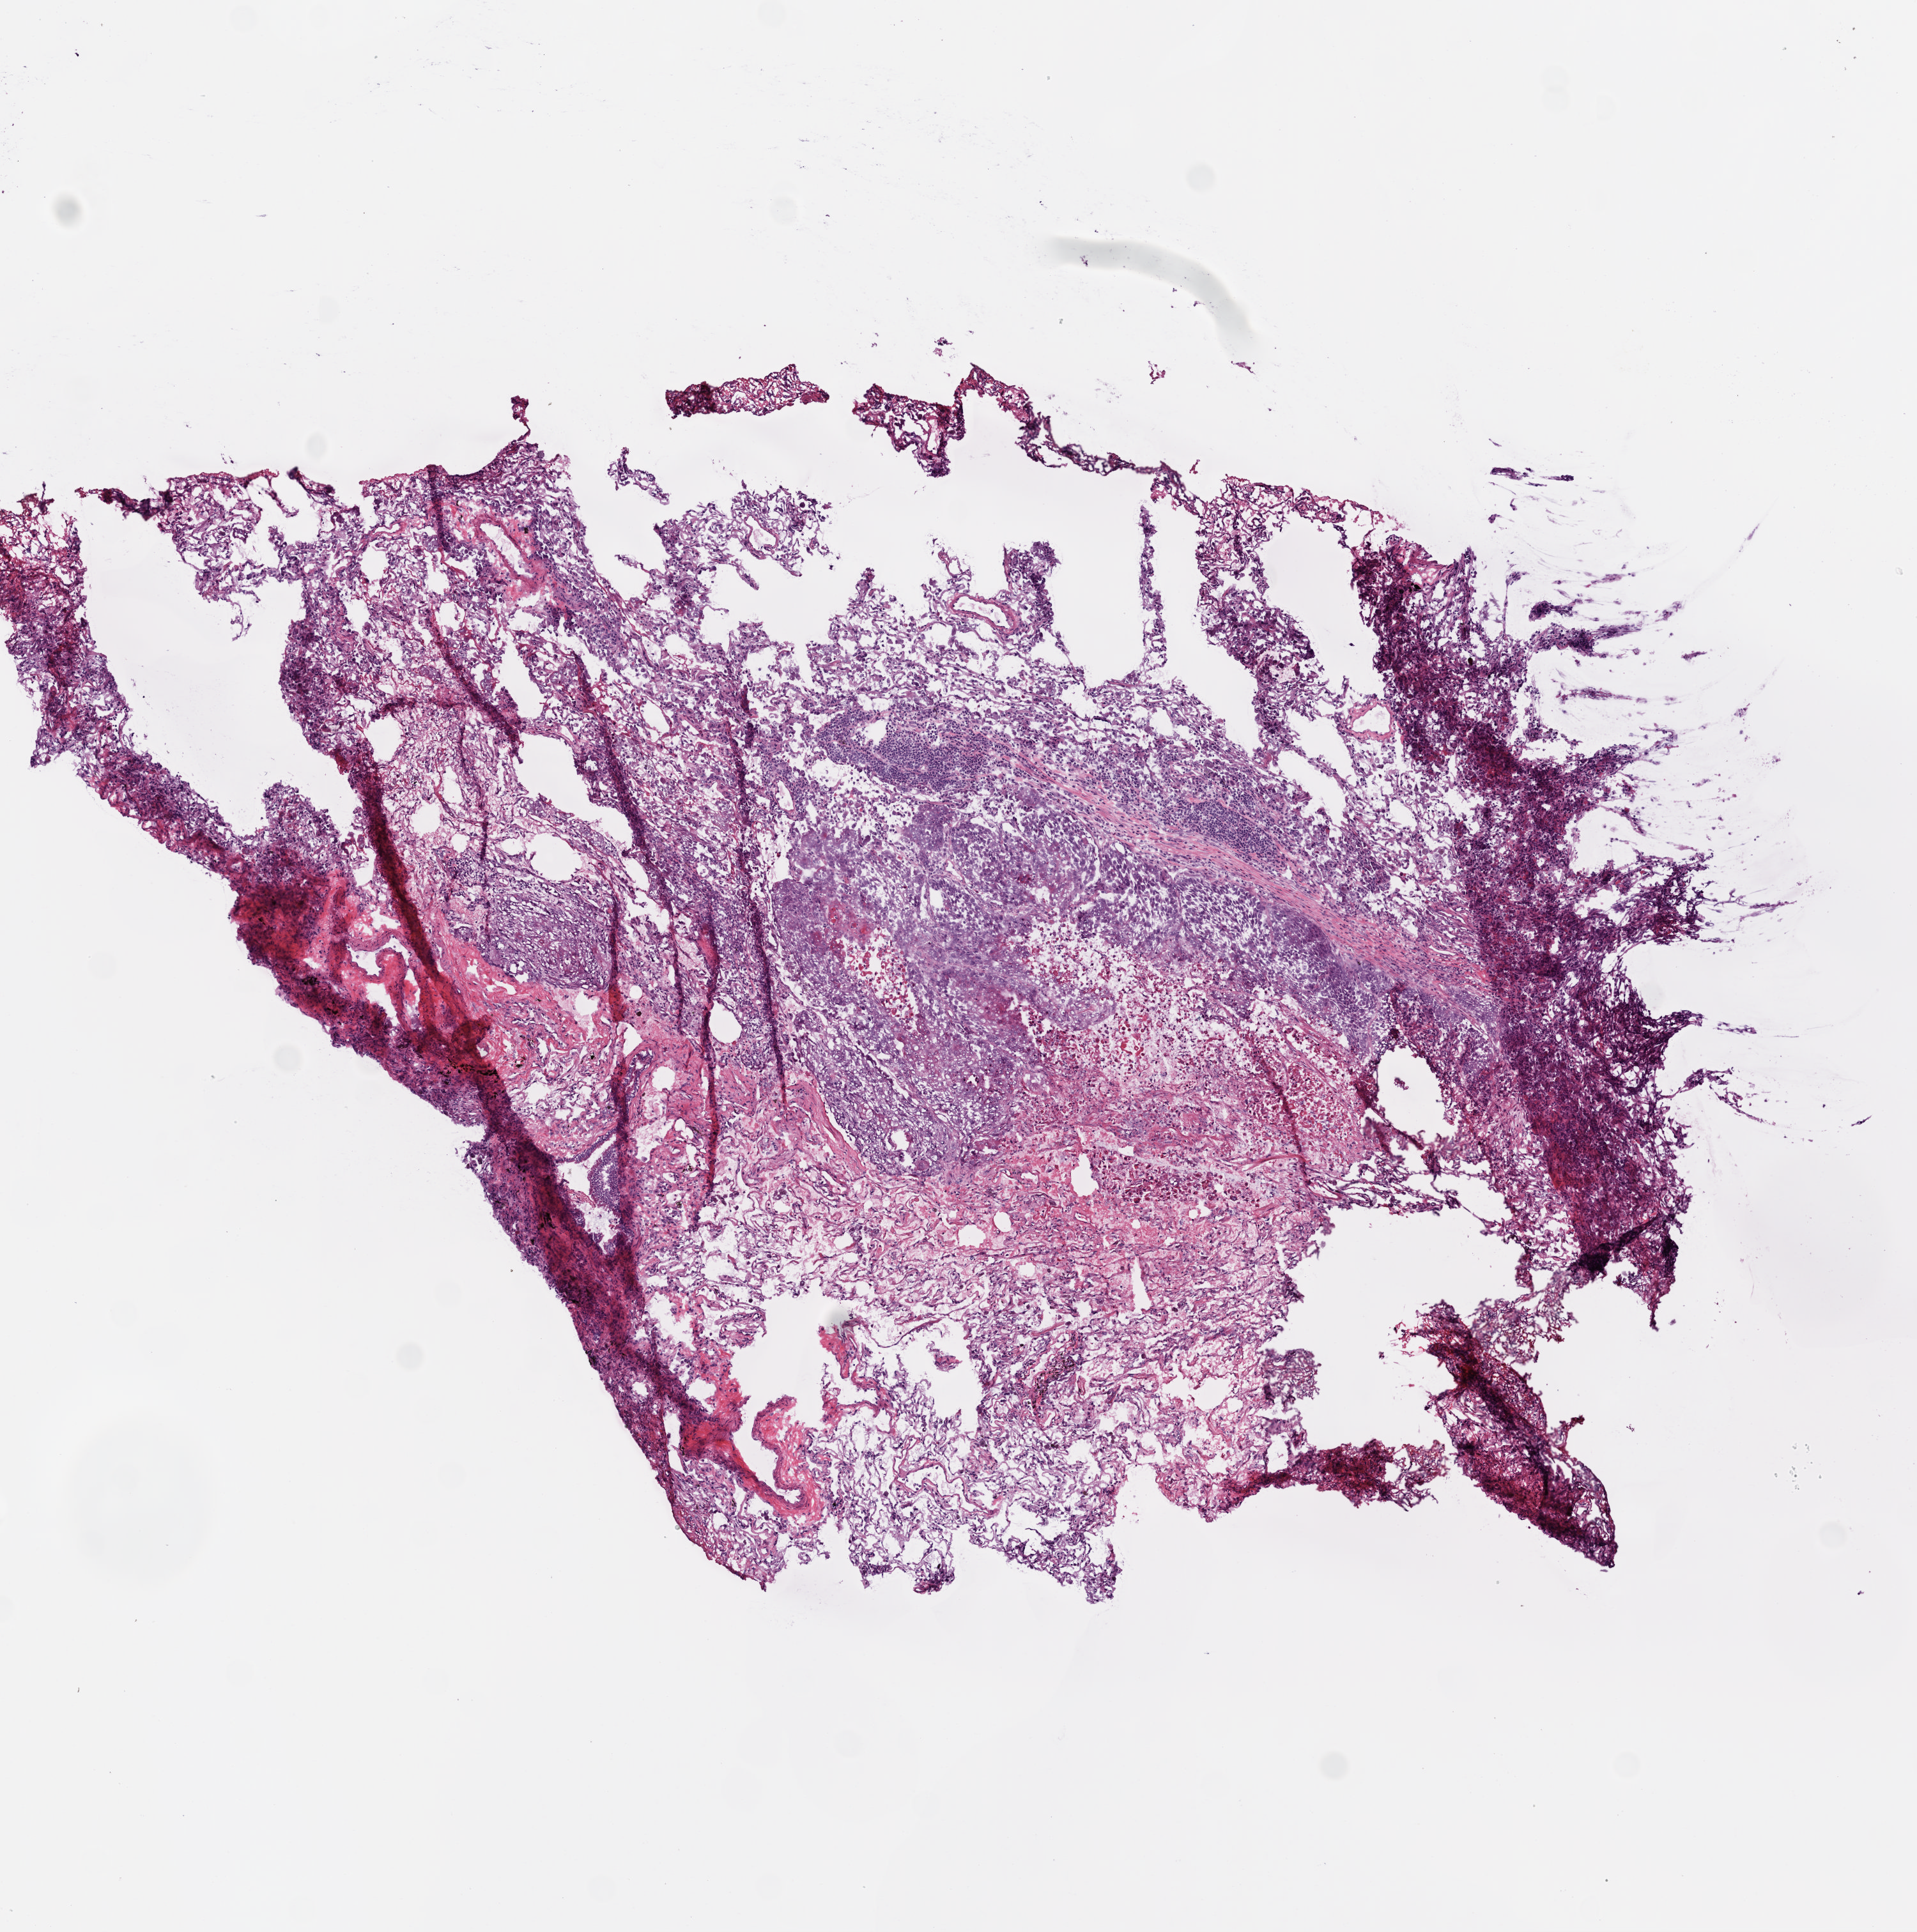
Whole-slide histology image, Hematoxylin and eosin (H&E) stained, whole scanned area (about 6.0 x 6.1 mm) shown as a low-resolution overview. Frozen section from the bottom of the tissue portion. Sample: primary tumour, lung. Male patient; age at initial diagnosis 51 years. Slide review estimates, as recorded: tumour cells 50%, tumour nuclei 70%, normal cells 40%, stromal cells 5%, necrosis 5%.
Diagnosis: Squamous cell carcinoma, NOS (upper lobe, lung). AJCC pathologic stage: IA. Laterality: left.